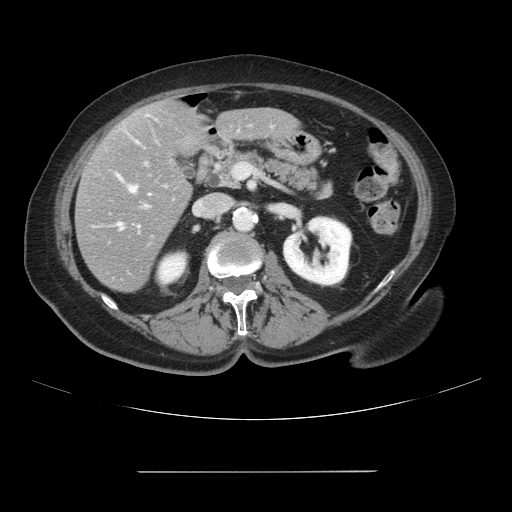
Contrast-enhanced abdominal CT, one axial slice; slice 40 of 111 in the series (ordered by position); intravenous contrast given; soft-tissue window (W 400 / L 40 HU); 512 × 512 image matrix, field of view 400 × 400 mm. Female patient, age 74 years. Case-level facts recorded for this patient, not image findings: diagnosis: colorectal cancer liver metastases, imaged before liver resection; multiple liver metastases: yes; largest metastasis: 1.1 cm; disease in both lobes: yes.
Structures marked on this image (expert manual segmentation):
- hepatic veins: bounding box (x1, y1, x2, y2) in pixels: (118, 186, 136, 229)
- liver: (76, 101, 299, 292)
- planned liver remnant (the part of the liver to remain after resection): (140, 101, 298, 155)
- portal vein (with intrahepatic branches): (116, 173, 147, 208)